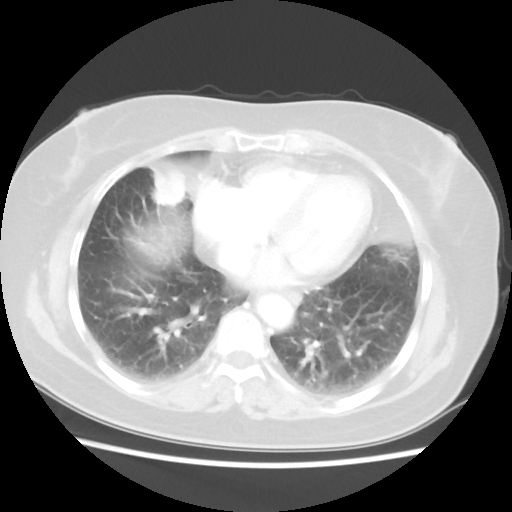
Chest CT, one axial slice. Slice 19 of 48 in the series (ordered by position). 100 kVp. Lung window (W 1500 / L -600 HU). 512 × 512 image matrix, field of view 343 × 343 mm. Patient: female, 61 years. Case-level facts recorded for this patient, not image findings: clinical TNM (as recorded): T1c N0 M0.
Annotated regions visible in this slice (bounding box drawn by a radiologist):
- lung tumour (recorded histology: adenocarcinoma): bounding box [x1, y1, x2, y2] px = [151, 162, 187, 208]